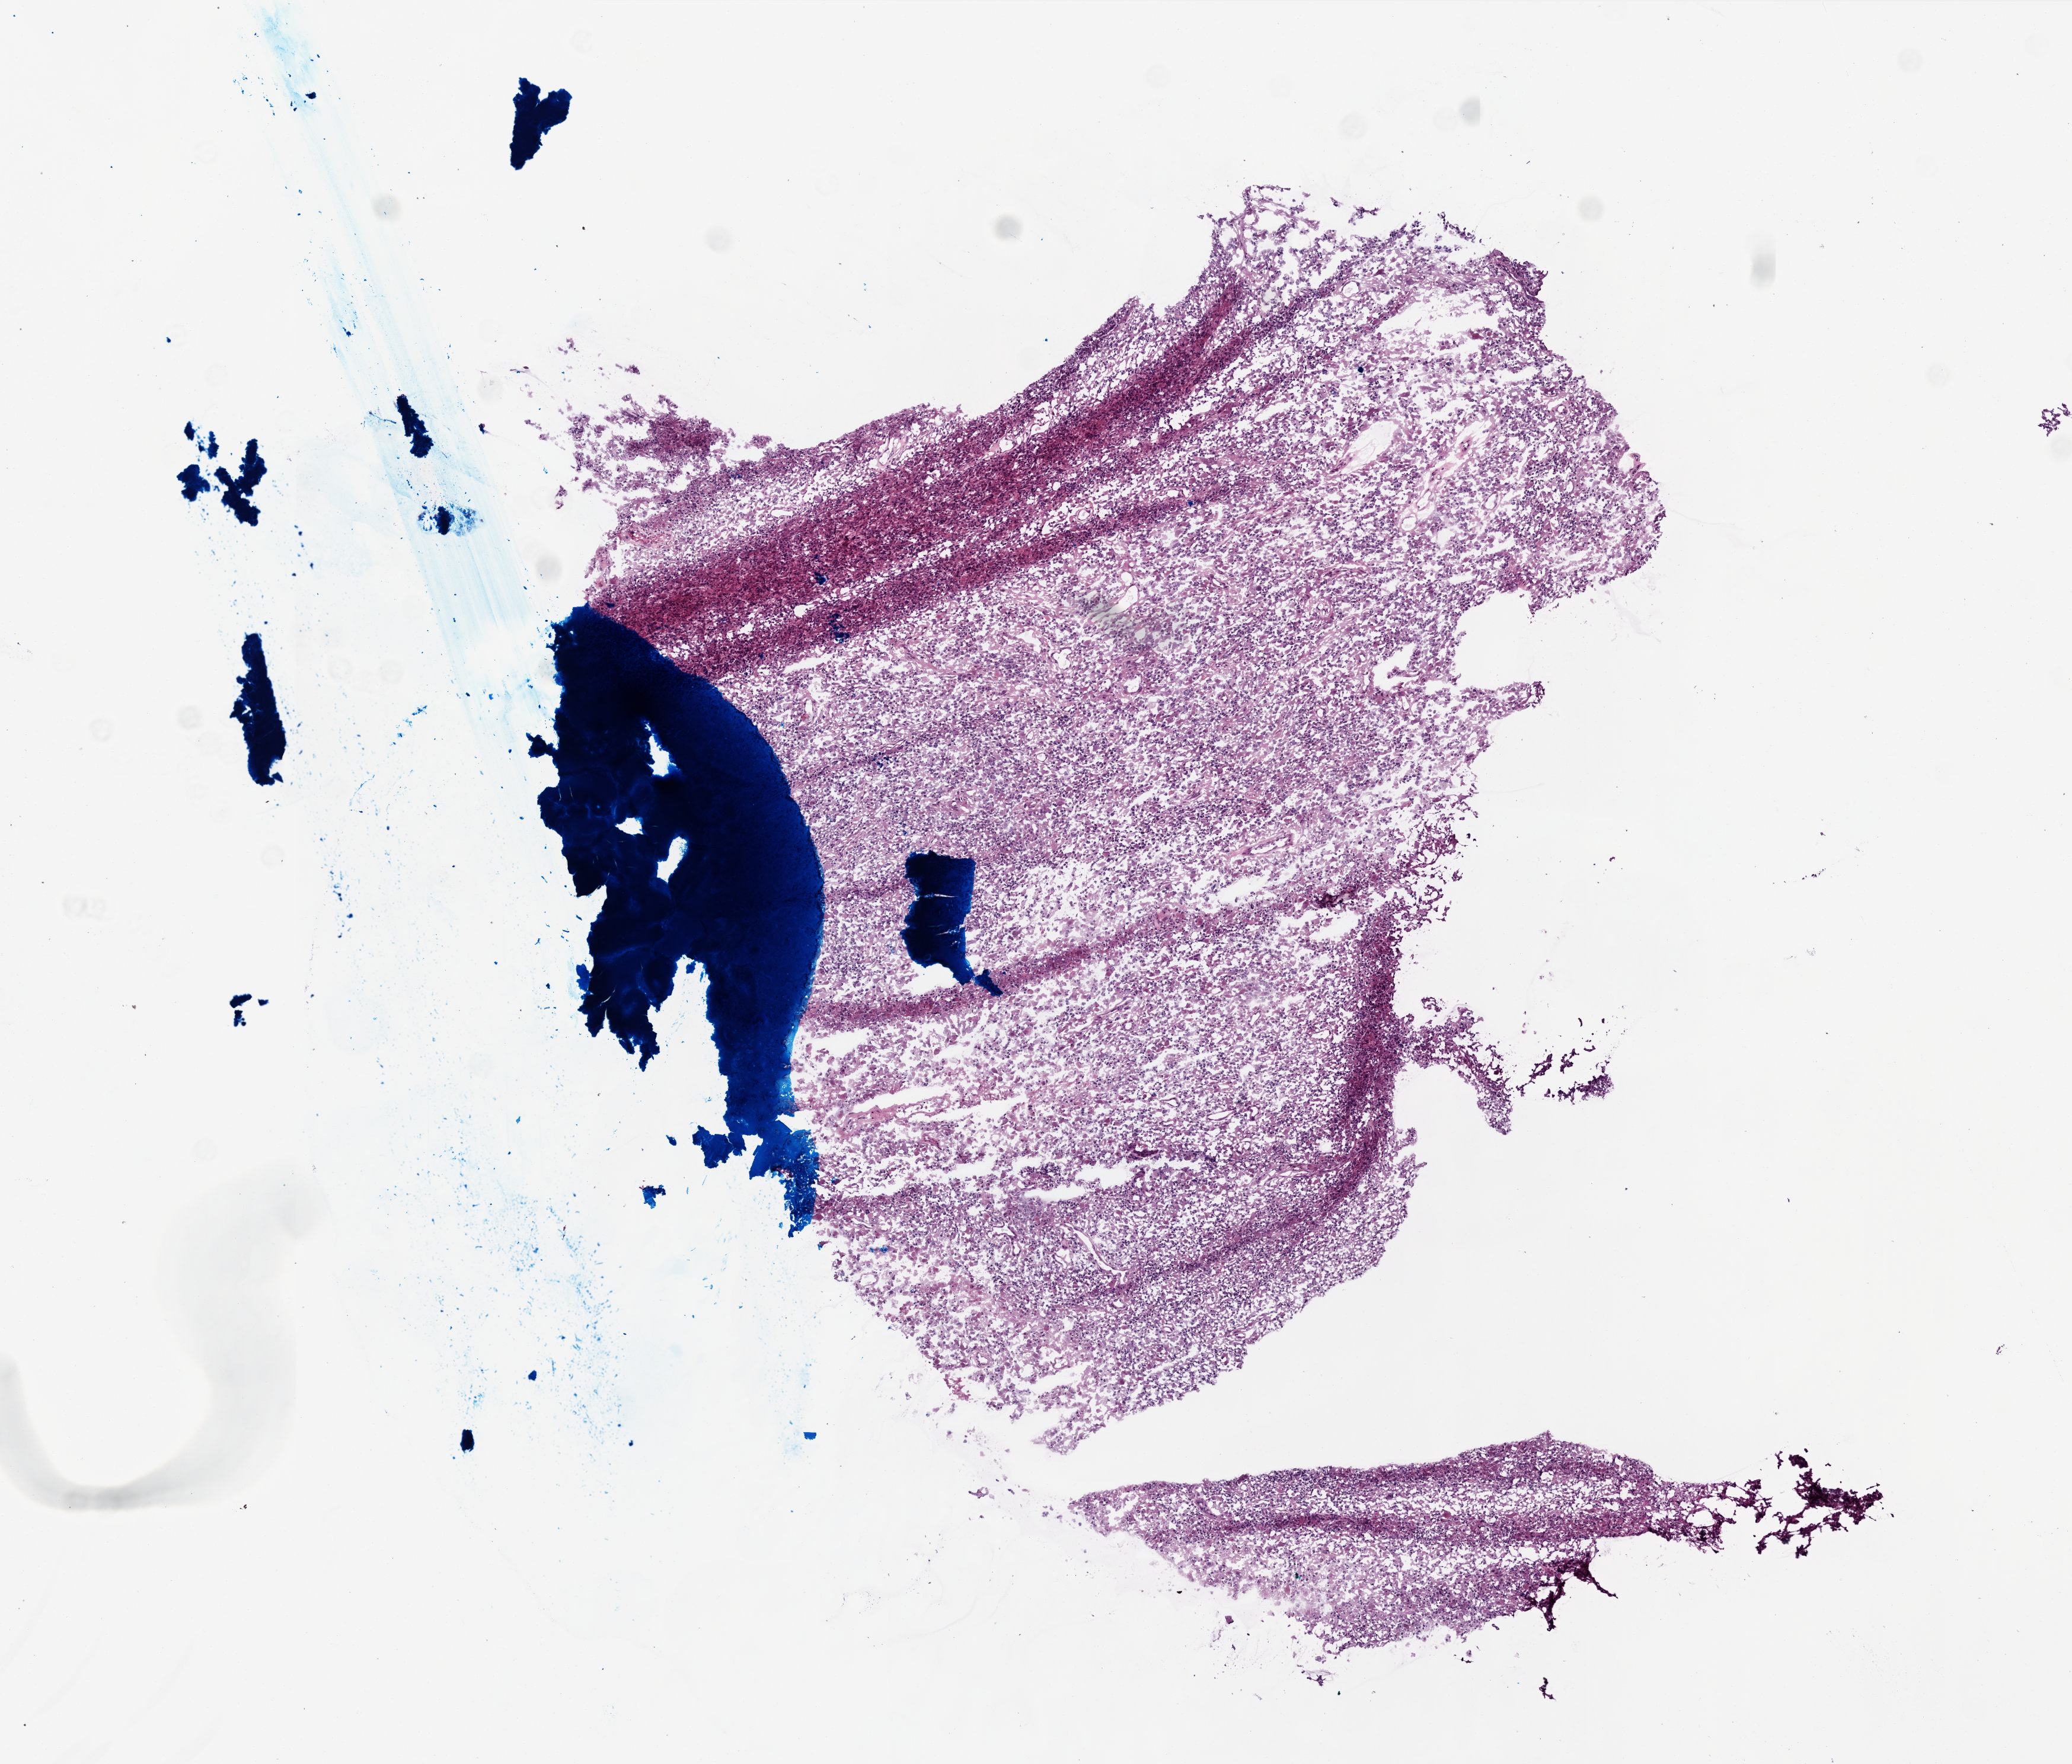
H&E whole-slide image — shown as a low-resolution overview of the whole scanned area (about 7.0 x 6.0 mm, slide scanned at 20x), frozen section, primary tumour sample from the brain. Female patient; age at initial diagnosis 34 years. Composition of this section per pathologist review: tumour cells 100%, tumour nuclei 100%, normal cells 0%, stromal cells 0%, necrosis 0%.
Histologic diagnosis: Glioblastoma.